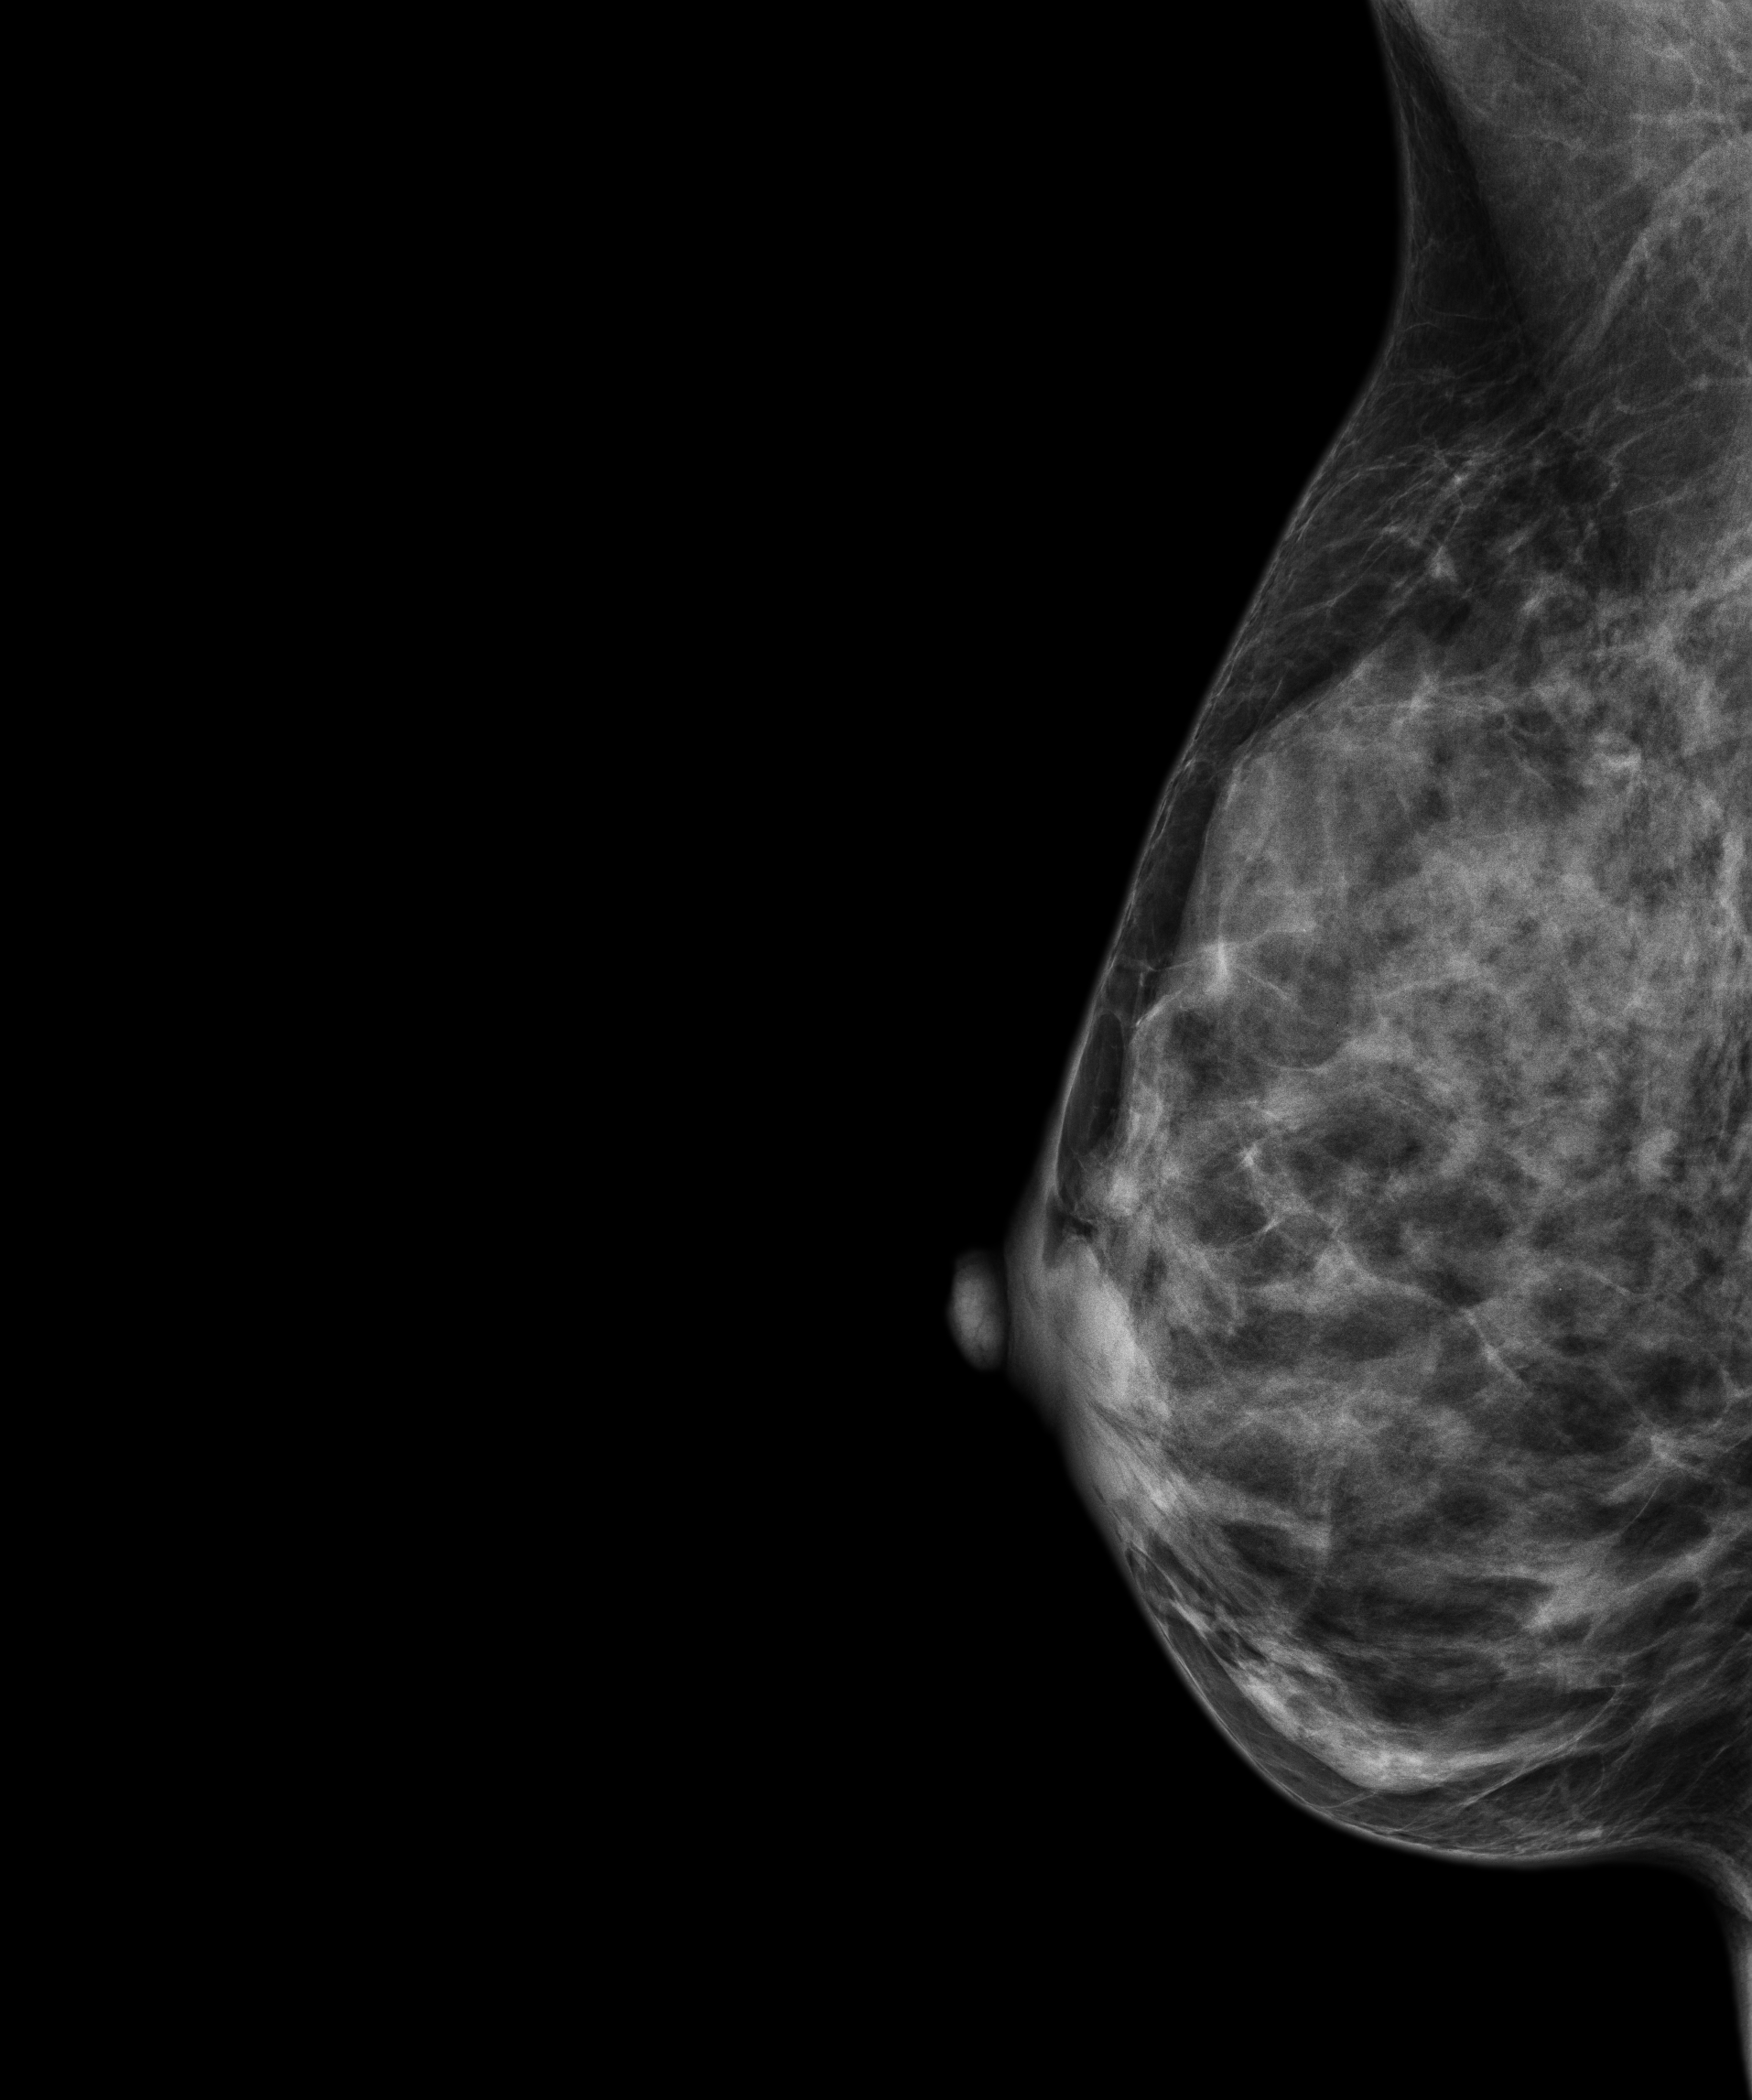
Full-field digital mammogram (FFDM); right breast; medio-lateral oblique projection; annual screening mammography examination. Patient: female, 45 years.
- breast density at the screening exam (both breasts): heterogeneously dense (BI-RADS density category c)
- final BI-RADS category for the screening round (tomosynthesis exam, both breasts): category 1
- recall: no recall after this screen